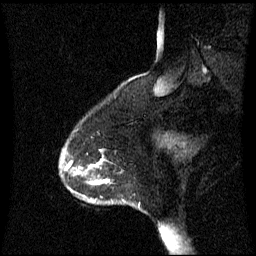
Breast MRI (dynamic contrast-enhanced), one sagittal slice. Slice 11 of 60 in the series (ordered by position). Dynamic contrast-enhanced series, image 2 of 3 at this slice position (ordered by acquisition). 1.5 T. TE 4.2 ms, TR 8.4 ms. 256 × 256 image matrix, field of view 240 × 240 mm. Female patient, age 45 years. Case-level facts recorded for this patient, not image findings: setting: breast cancer imaged before/during neoadjuvant chemotherapy; receptor status: HR-positive, HER2-negative.
Structures marked on this image (semi-automatically segmented with operator editing):
- analysis volume of interest (the breast-tissue region the enhancement analysis was run in; not a lesion): box from (x=60, y=150) to (x=109, y=203) px
- tumour enhancement mask (voxels above the 70 % enhancement threshold inside the analysis volume of interest): (x=96, y=180)–(x=109, y=185)